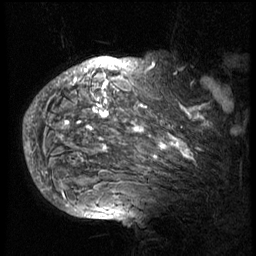
Breast MRI (dynamic contrast-enhanced), one sagittal slice; slice 57 of 74 in the series (ordered by position); 3 images stored at this slice position (order not interpretable as contrast timing); 1.5 T; TE 4.2 ms, TR 8.9 ms; 2.5 mm slice thickness; 256 × 256 image matrix, field of view 200 × 200 mm. Patient: female, 57 years. From the clinical record (not read from this slice): setting: breast cancer imaged before/during neoadjuvant chemotherapy; receptor status: HER2-positive.
Outlined on this slice (semi-automatically segmented with operator editing):
- analysis volume of interest (the breast-tissue region the enhancement analysis was run in; not a lesion): bounding box (x1, y1, x2, y2) in pixels: (40, 62, 241, 175)
- tumour enhancement mask (voxels above the 140 % enhancement threshold inside the analysis volume of interest): (40, 62, 210, 175)